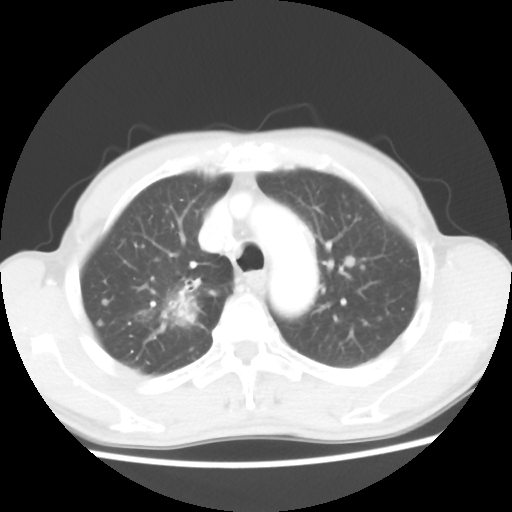
Chest CT, one axial slice; slice 40 of 52 in the series (ordered by position); 100 kVp; lung window (W 1500 / L -600 HU); 5 mm slice thickness; 512 × 512 image matrix. Male patient, age 66 years. Case-level facts recorded for this patient, not image findings: clinical TNM (as recorded): T2 N0 M1a.
Outlined on this slice (rectangle marked by the reading radiologist):
- lung tumour (recorded histology: adenocarcinoma): bounding box (x1, y1, x2, y2) in pixels: (147, 274, 219, 334)